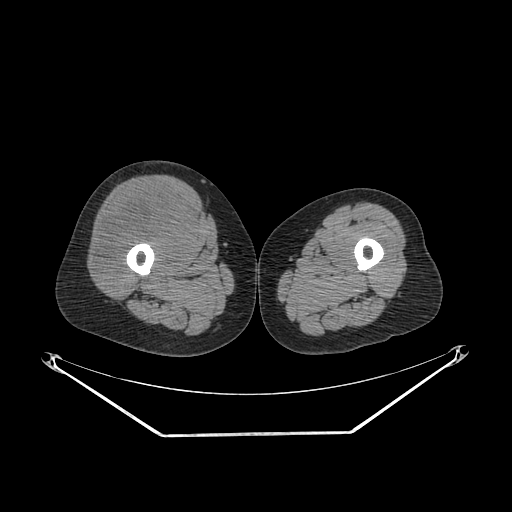
CT of an extremity soft-tissue mass (from a PET/CT study), one axial slice. Position 241 of 311 along the scan axis. Reconstruction kernel SOFT. Soft-tissue window (W 400 / L 40 HU). 3.75 mm slice thickness. 512 × 512 image matrix, field of view 500 × 500 mm. Female patient. Case-level facts recorded for this patient, not image findings: histological type: pleiomorphic undifferentiated sarcoma; grade: high; site of the primary tumour: right quadricep.
Annotated regions visible in this slice (expert contour drawn on MRI and transferred to this co-registered scan by the dataset authors):
- tumour plus oedema (research contour): bounding box (x1, y1, x2, y2) in pixels: (98, 190, 193, 282)
- tumour (research contour): (98, 190, 193, 282)